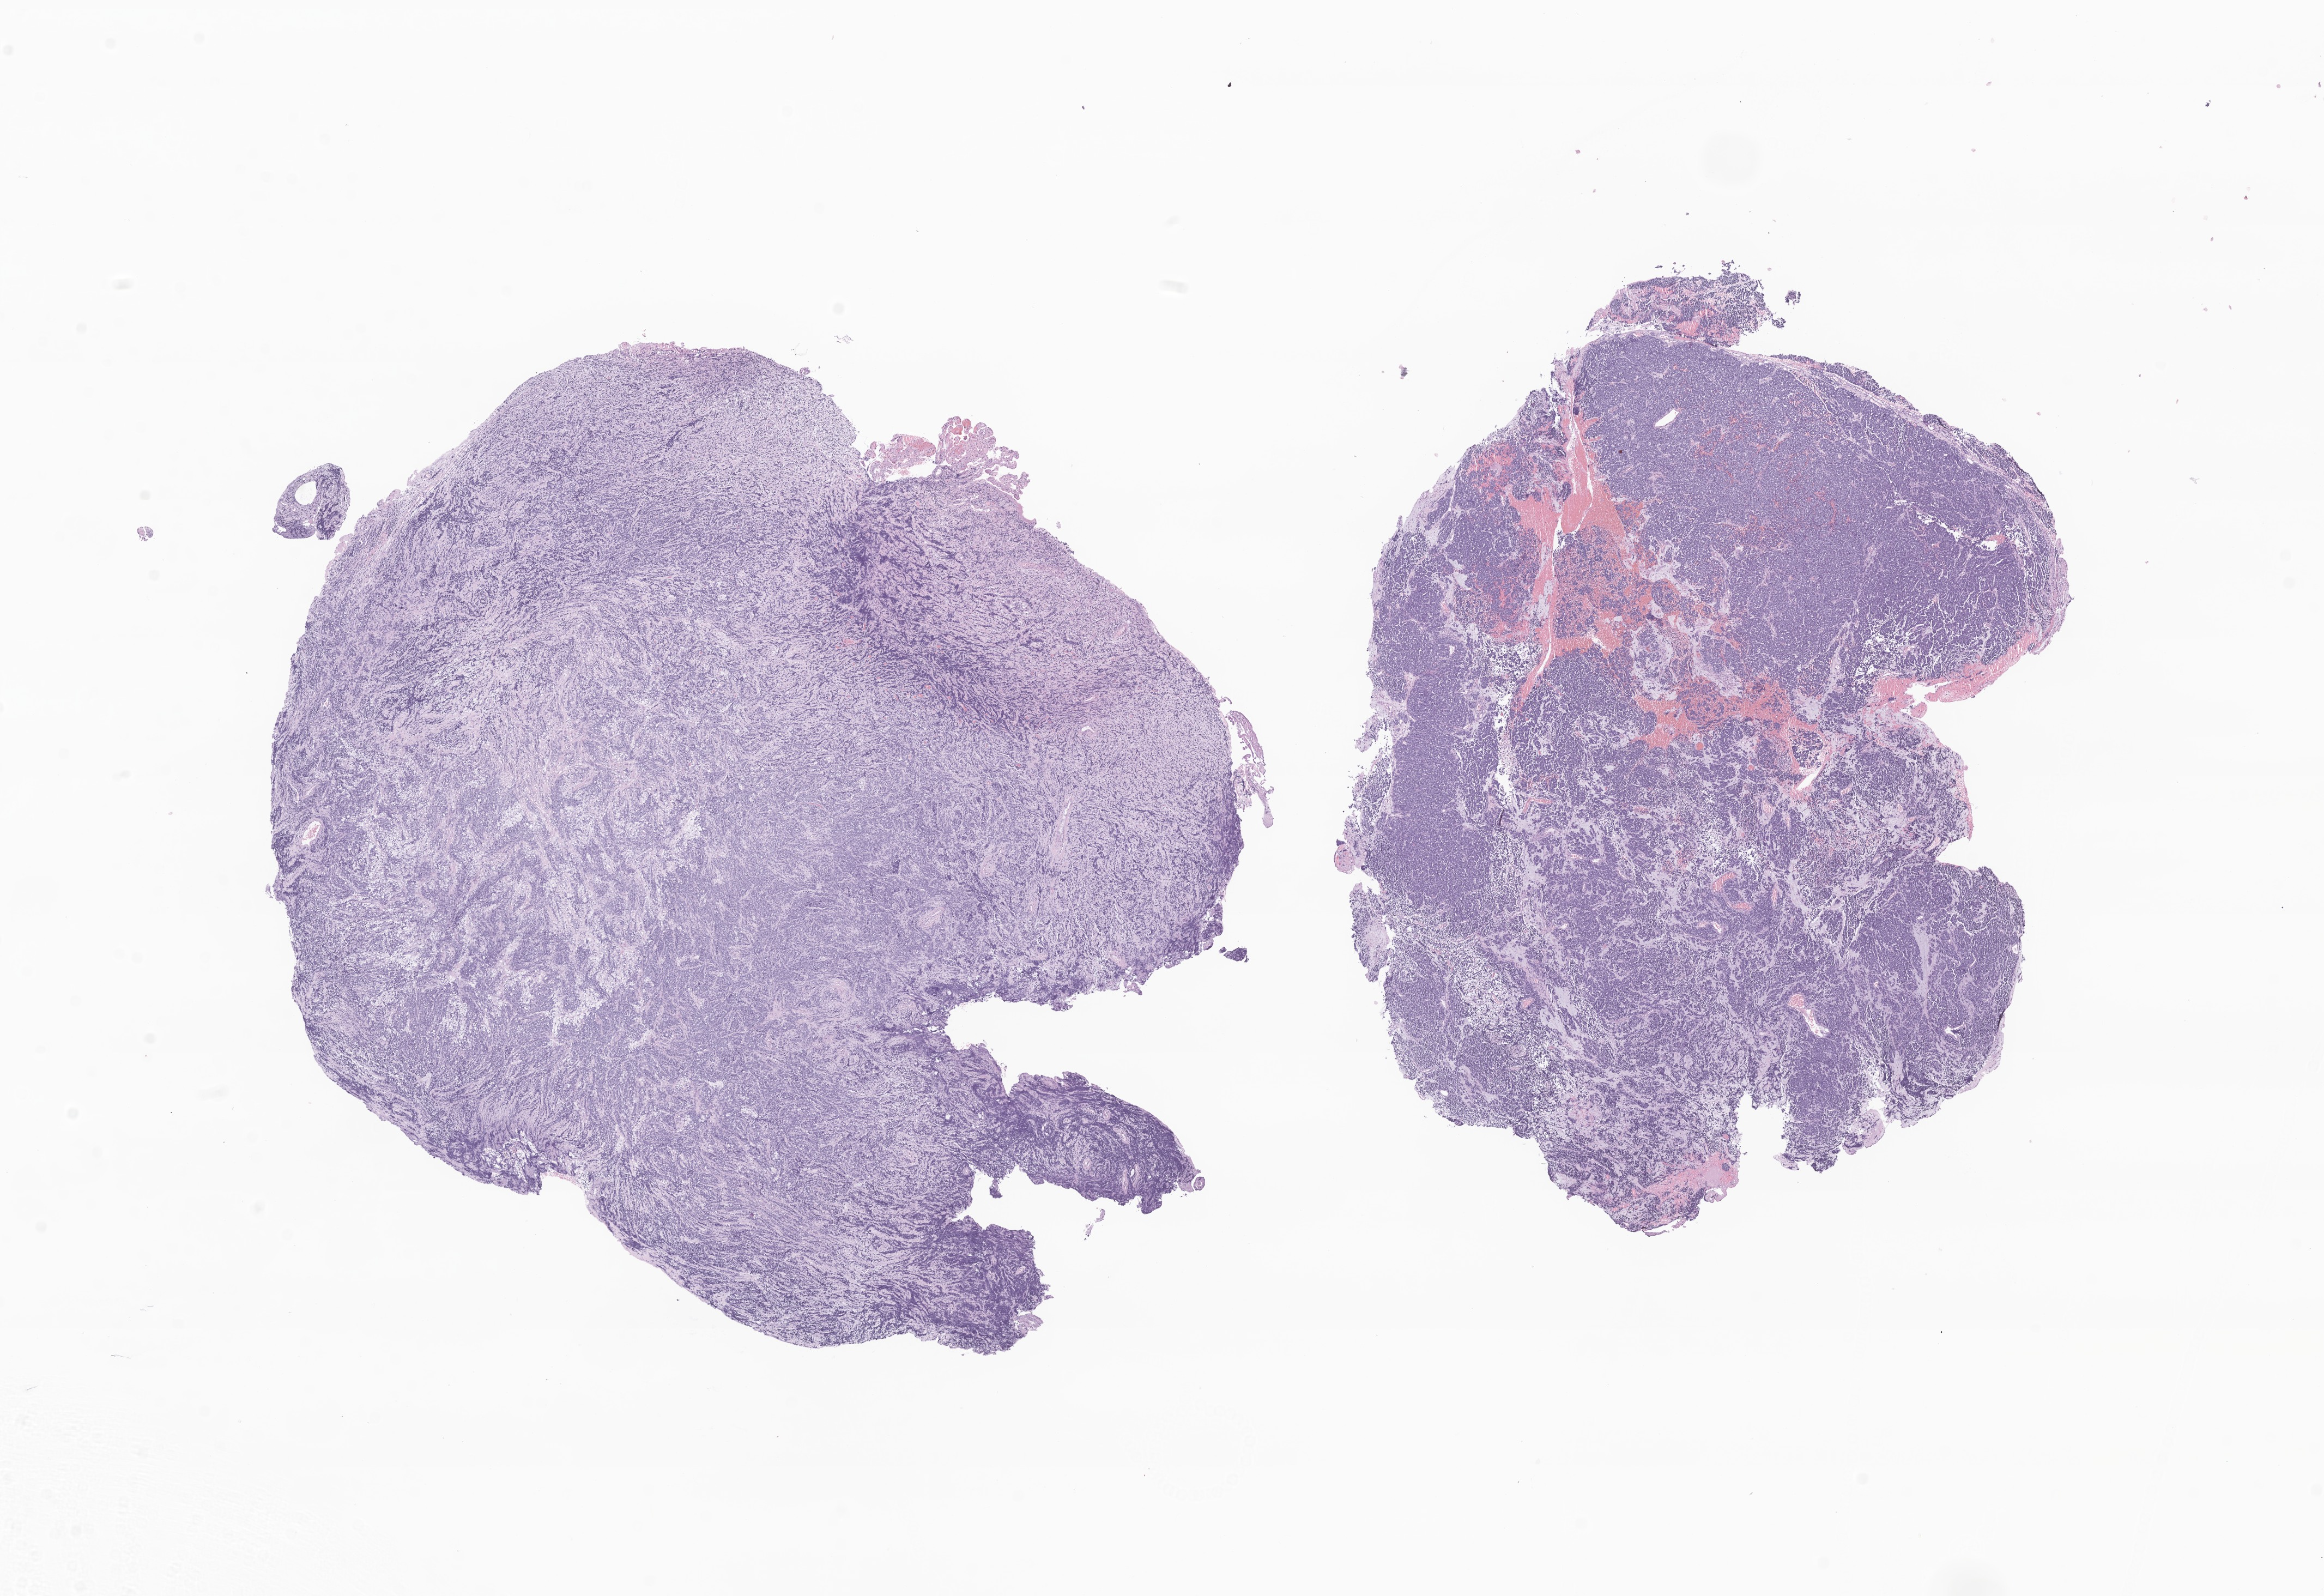
Hematoxylin and eosin (H&E) whole-slide image of tumor tissue from the brain — shown as a low-resolution overview of the whole scanned area (about 18.0 x 12.3 mm), formalin-fixed paraffin-embedded section. Patient male; age 82 months (6 years 10 months).
Recorded diagnosis: Medulloblastoma, NOS.